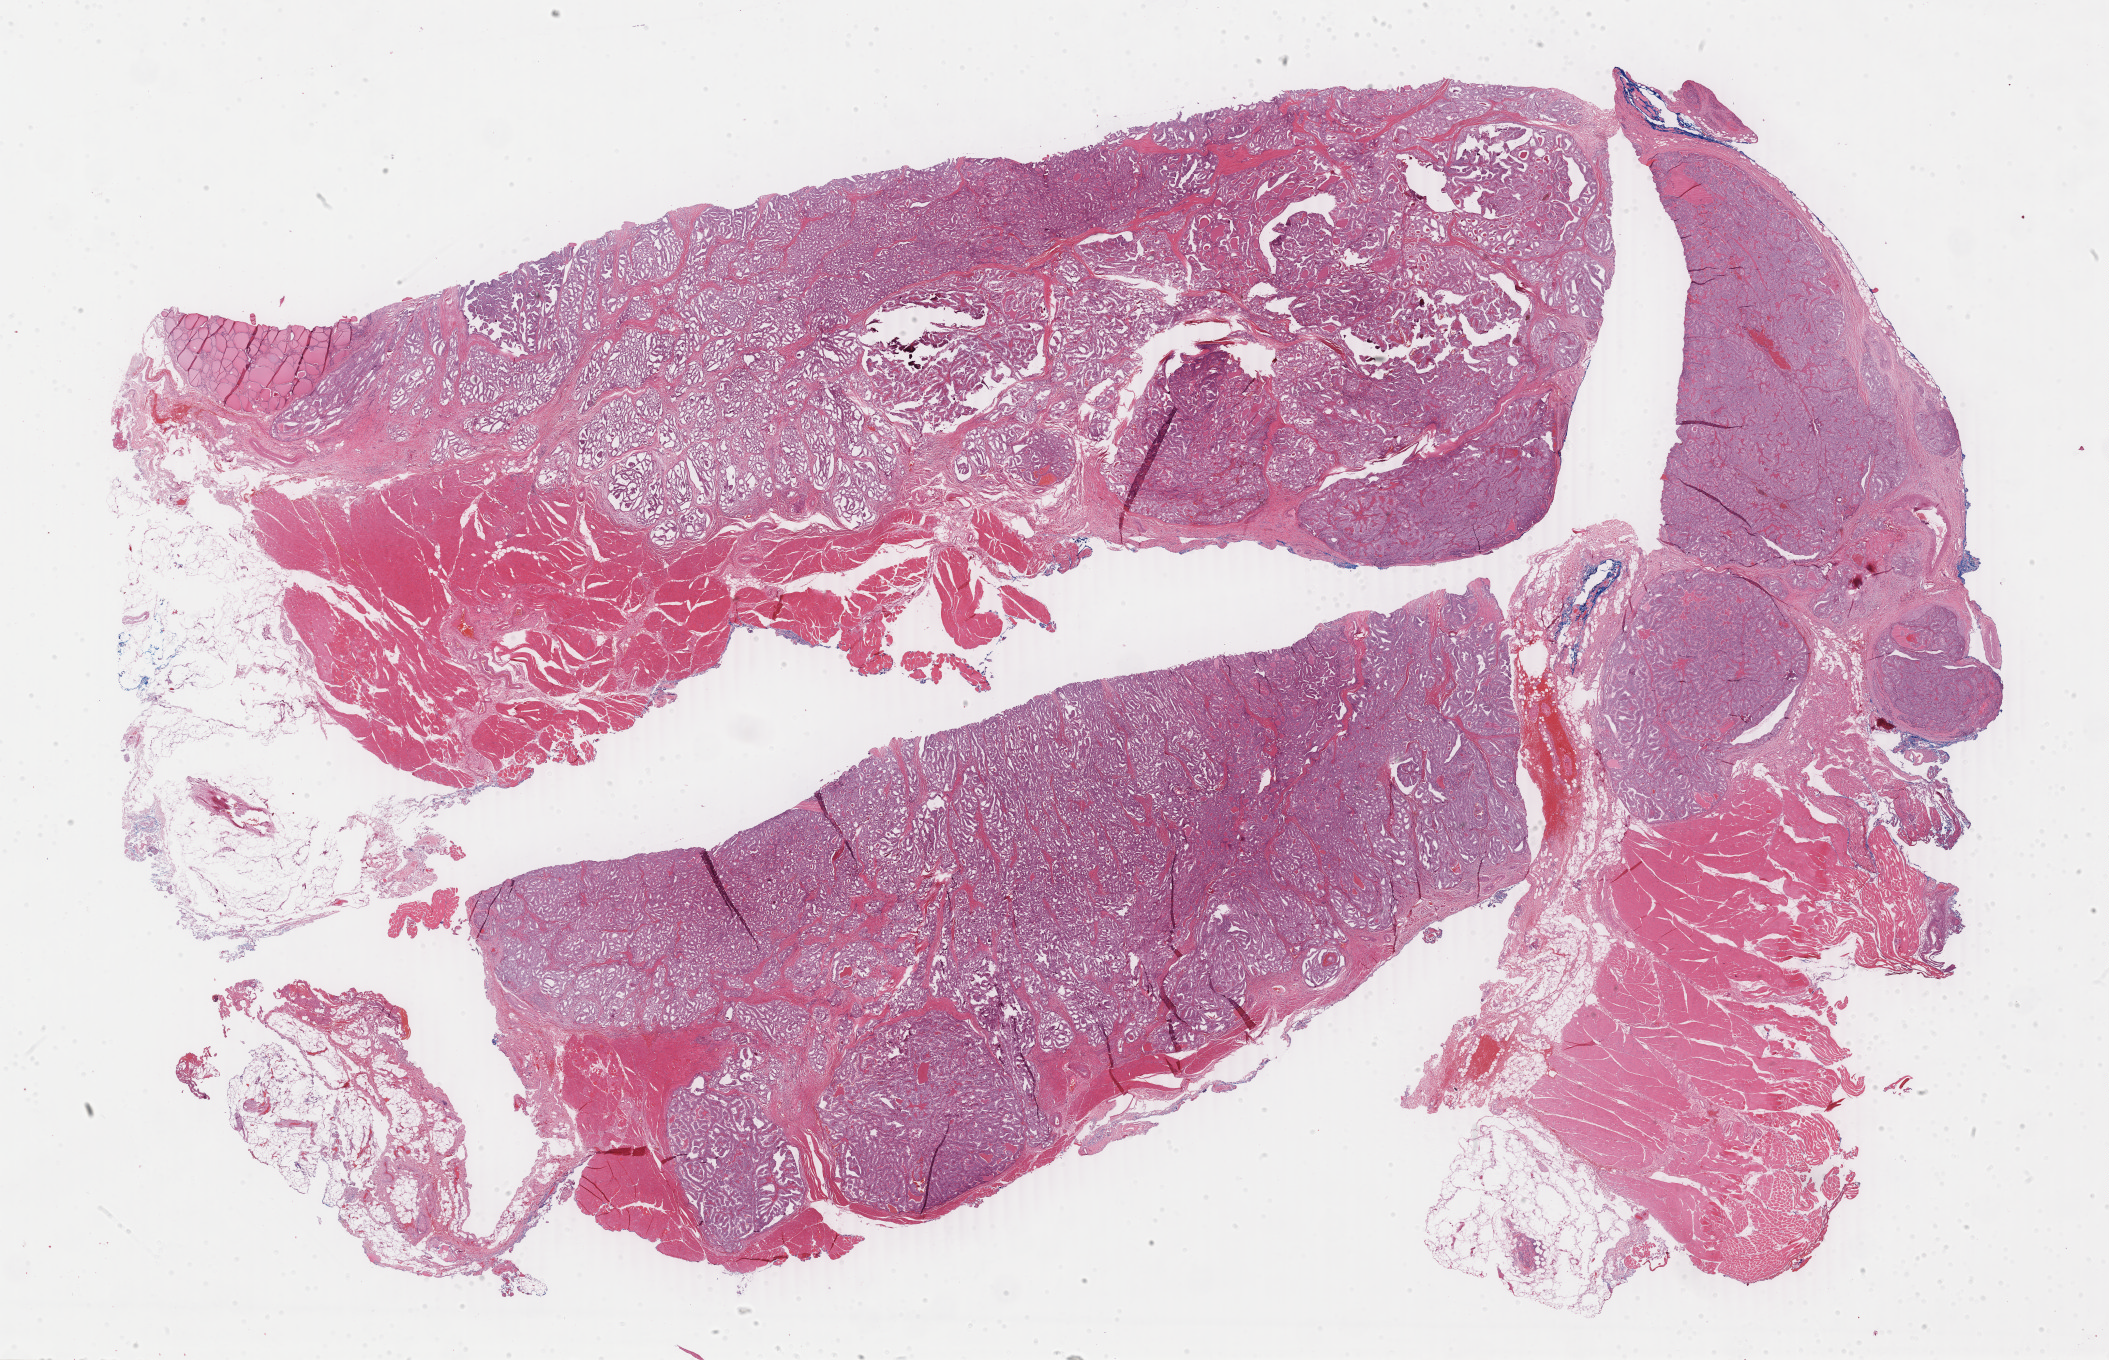
H&E whole-slide image, shown as a low-resolution overview of the whole scanned area (about 33.6 x 21.6 mm, slide scanned at 40x); formalin-fixed paraffin-embedded (FFPE) diagnostic section; sample: primary tumour, thyroid. Male patient; age at initial diagnosis 70 years.
Laterality: left. TNM: T3 N1a M0. Lymph nodes positive (case pathology): 3 of 3 examined. AJCC pathologic stage: III. Histologic diagnosis: Papillary carcinoma, columnar cell (thyroid gland).